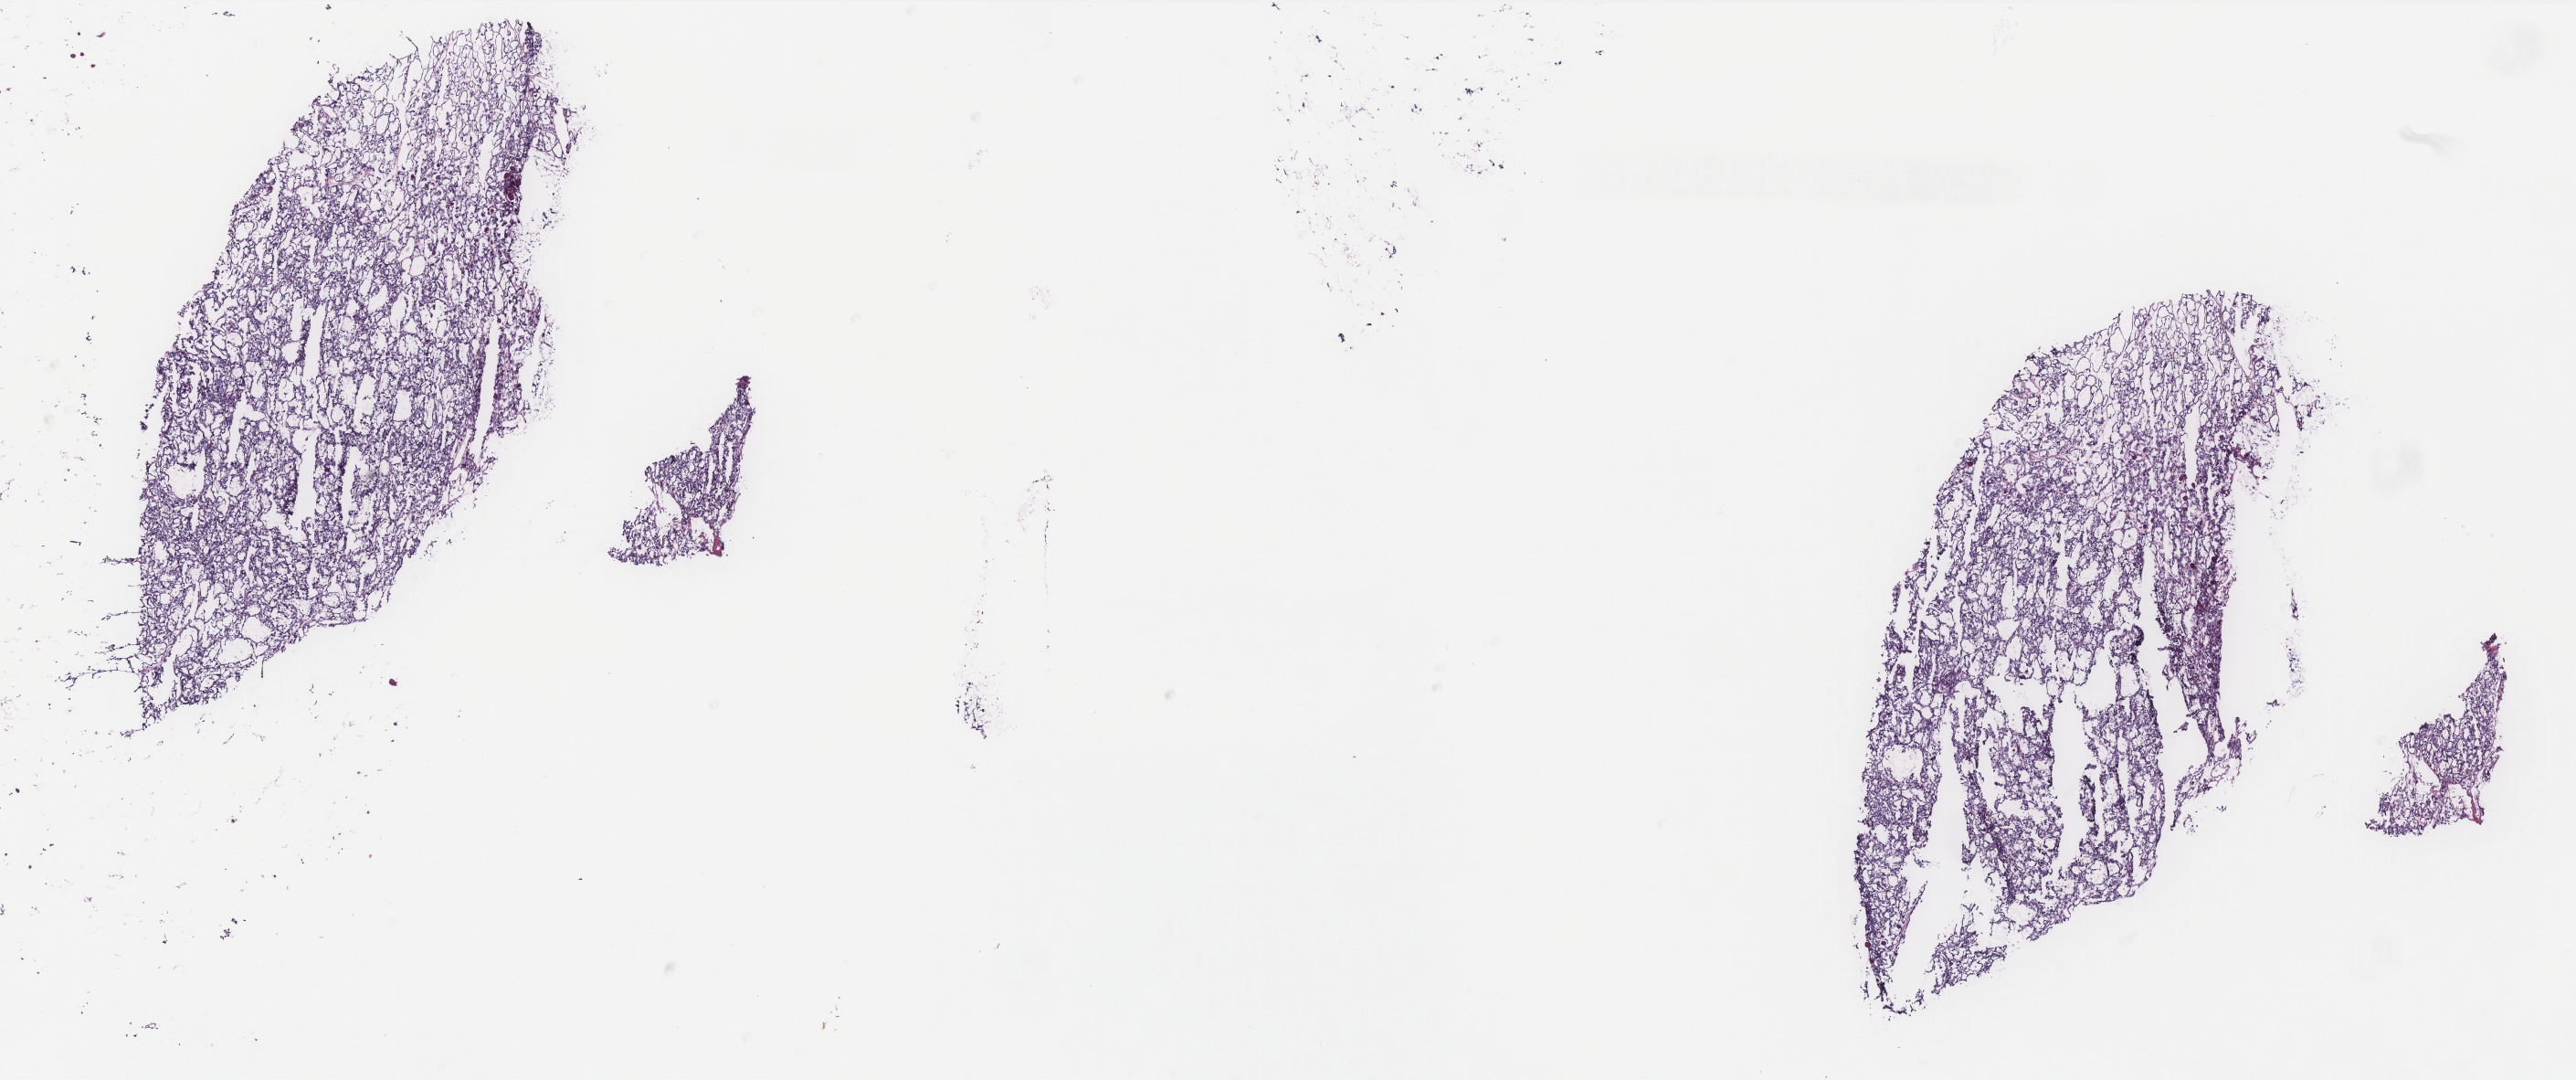
Whole-slide histology image, Hematoxylin and eosin (H&E) stained, a low-resolution overview of the entire scanned area, about 22.6 x 9.5 mm (acquisition: 40x scan), frozen section from the bottom of the tissue portion, thyroid, primary tumour sample. Female, age 63 years at initial diagnosis.
Diagnosis: Papillary adenocarcinoma, NOS.